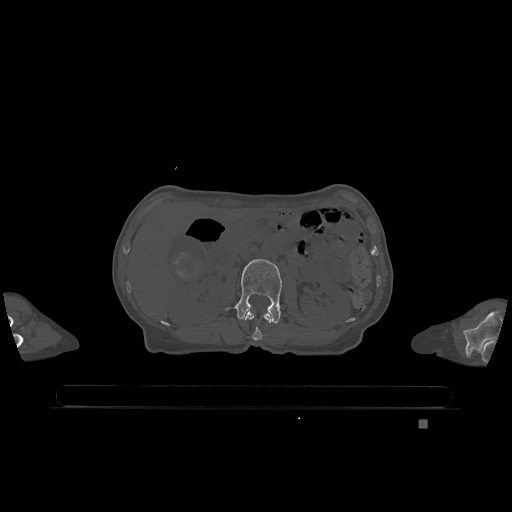
CT including the spine, one axial slice. Position 432 of 1317 along the scan axis. Bone window (W 1800 / L 400 HU). 0.5 mm slice thickness. 512 × 512 image matrix, field of view 500 × 500 mm. Patient: female, 74 years. From the clinical record (not read from this slice): primary cancer: lung; vertebrae with lytic lesions (as recorded): T1, T4, T5, T6, L4, L5.
Annotated regions visible in this slice (semi-automatic segmentation, software-assisted and operator-edited):
- L1 vertebra: box from (x=244, y=311) to (x=272, y=341) px
- L2 vertebra: (x=235, y=259)–(x=282, y=323)